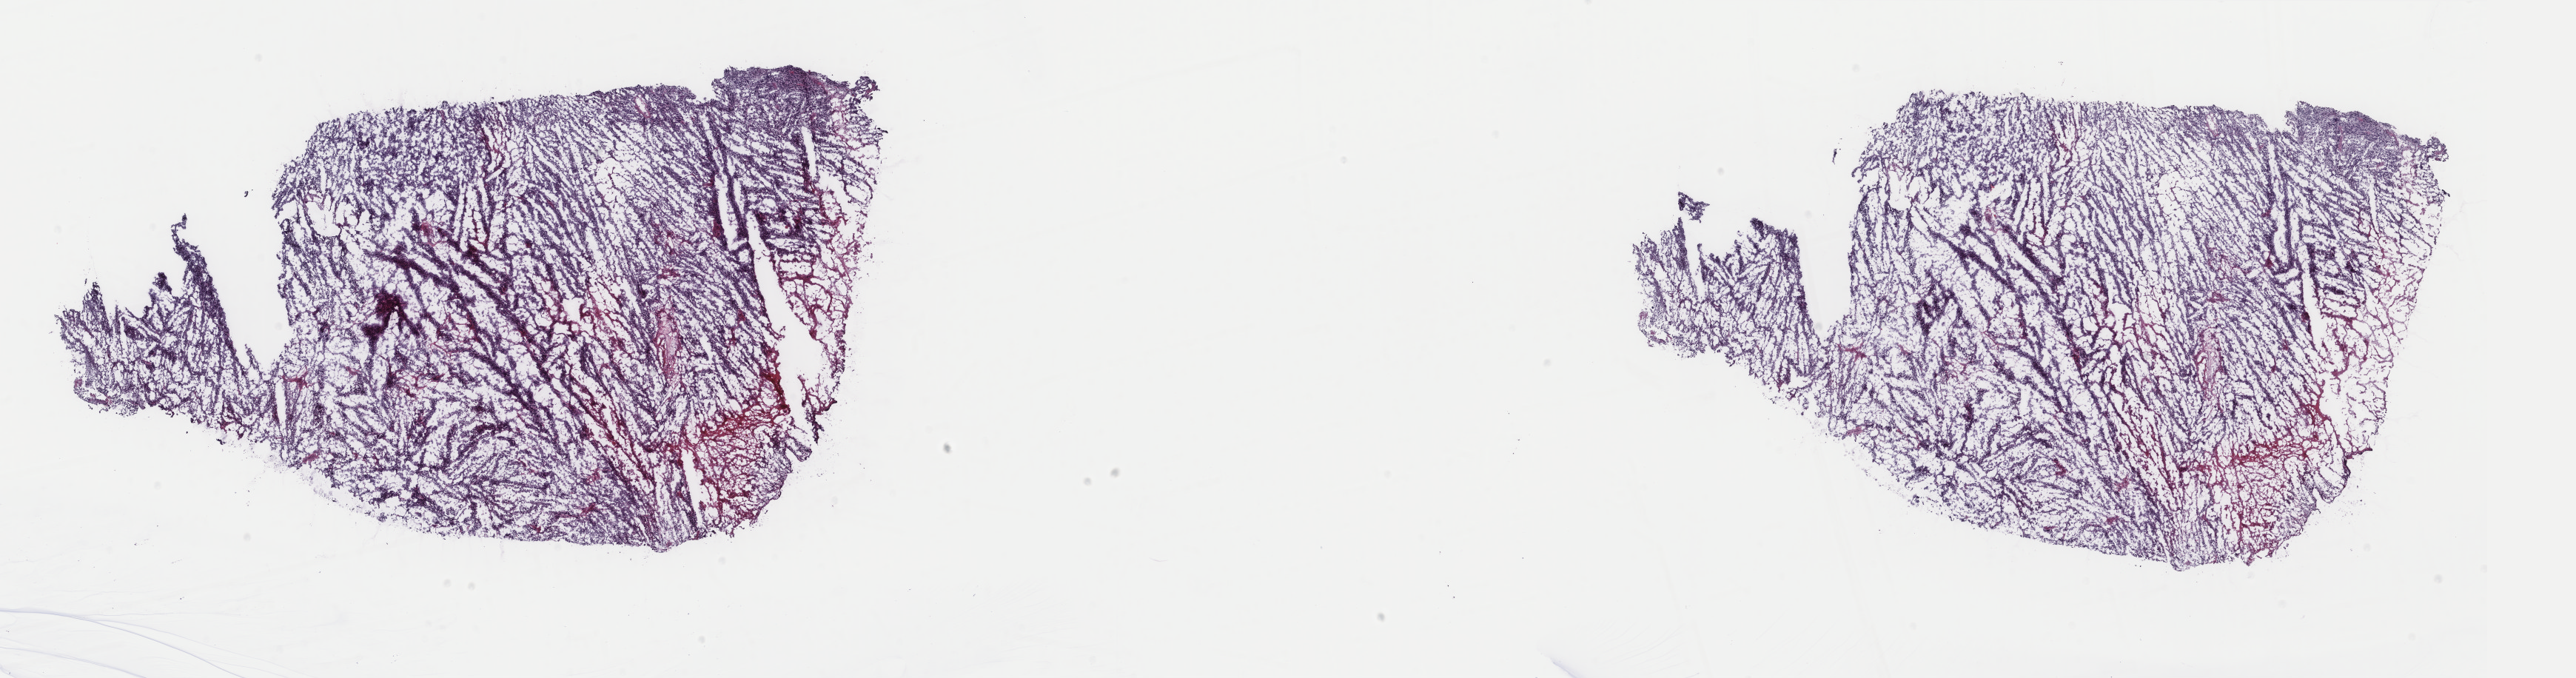
Whole-slide histology image, Hematoxylin and eosin (H&E) stained, low-resolution overview of the scanned area, about 27.6 x 7.3 mm. Frozen section. Sample: primary tumour, uterus. Female patient; age at initial diagnosis 67 years. Pathologist review of this section (percent, as recorded): tumour cells 60%, tumour nuclei 60%, normal cells 30%, stromal cells 5%, necrosis 5%. Inflammatory infiltration, as recorded: lymphocyte infiltration 50%, monocyte infiltration 20%, neutrophil infiltration 5%.
• FIGO stage: IIIC2
• histologic diagnosis: Mullerian mixed tumor